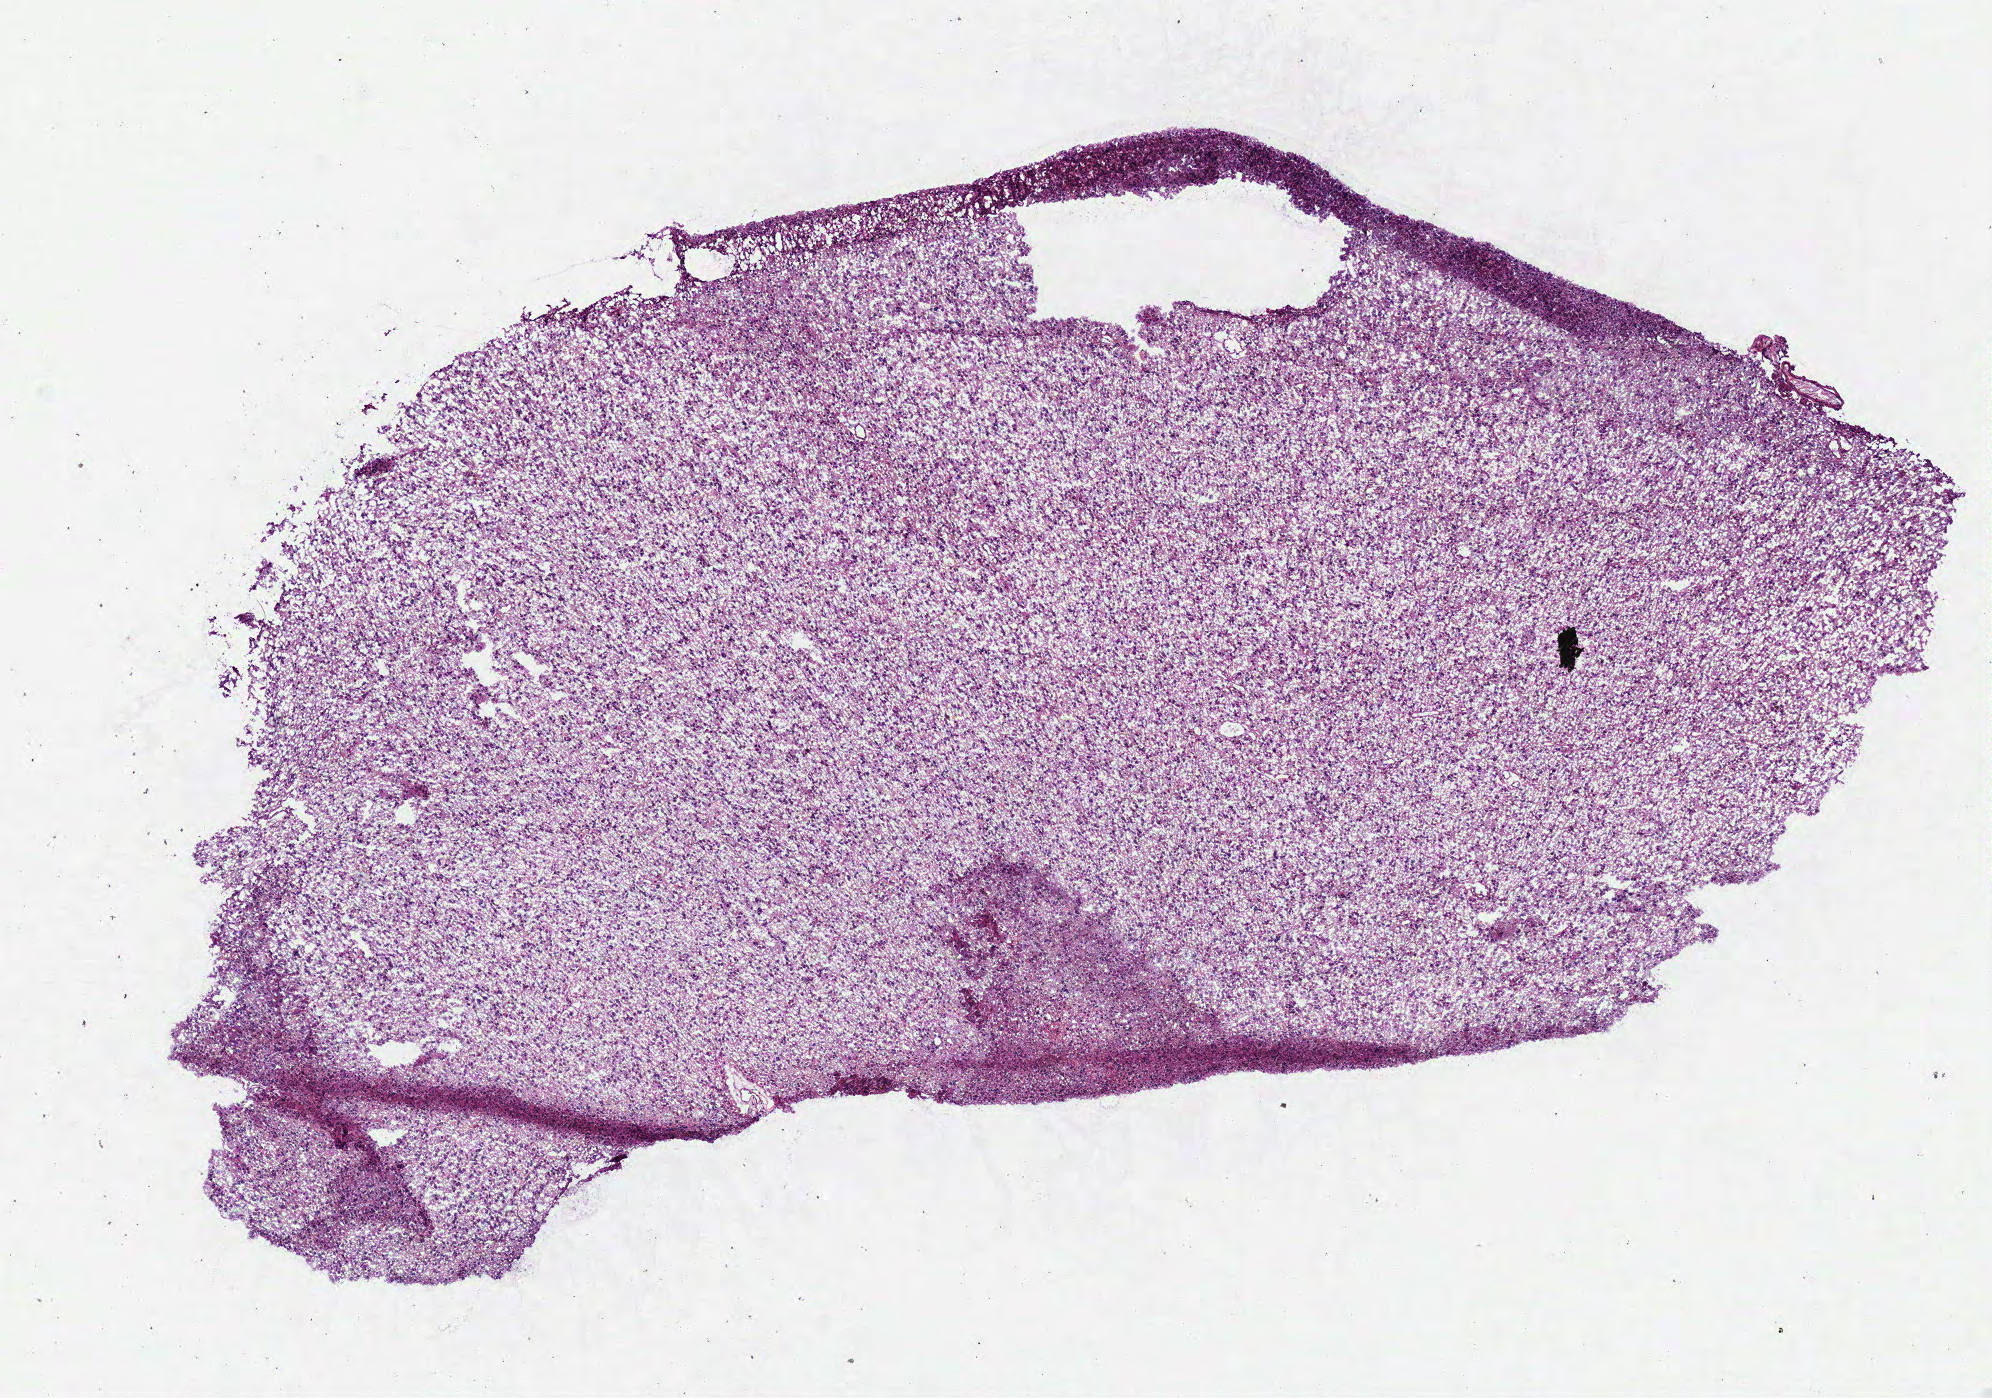
Digitized Hematoxylin and eosin (H&E) stained tissue section (whole slide), a low-resolution overview of the entire scanned area, about 7.8 x 5.5 mm (from a 40x scan), frozen section, primary tumour sample from the brain. Female, age 23 years at initial diagnosis. Histologic grade: G3 (poorly differentiated). Composition of this section per pathologist review: tumour cells 100%, tumour nuclei 75%, normal cells 0%, stromal cells 0%, necrosis 0%.
Pathologic diagnosis: Oligodendroglioma, anaplastic (cerebrum).